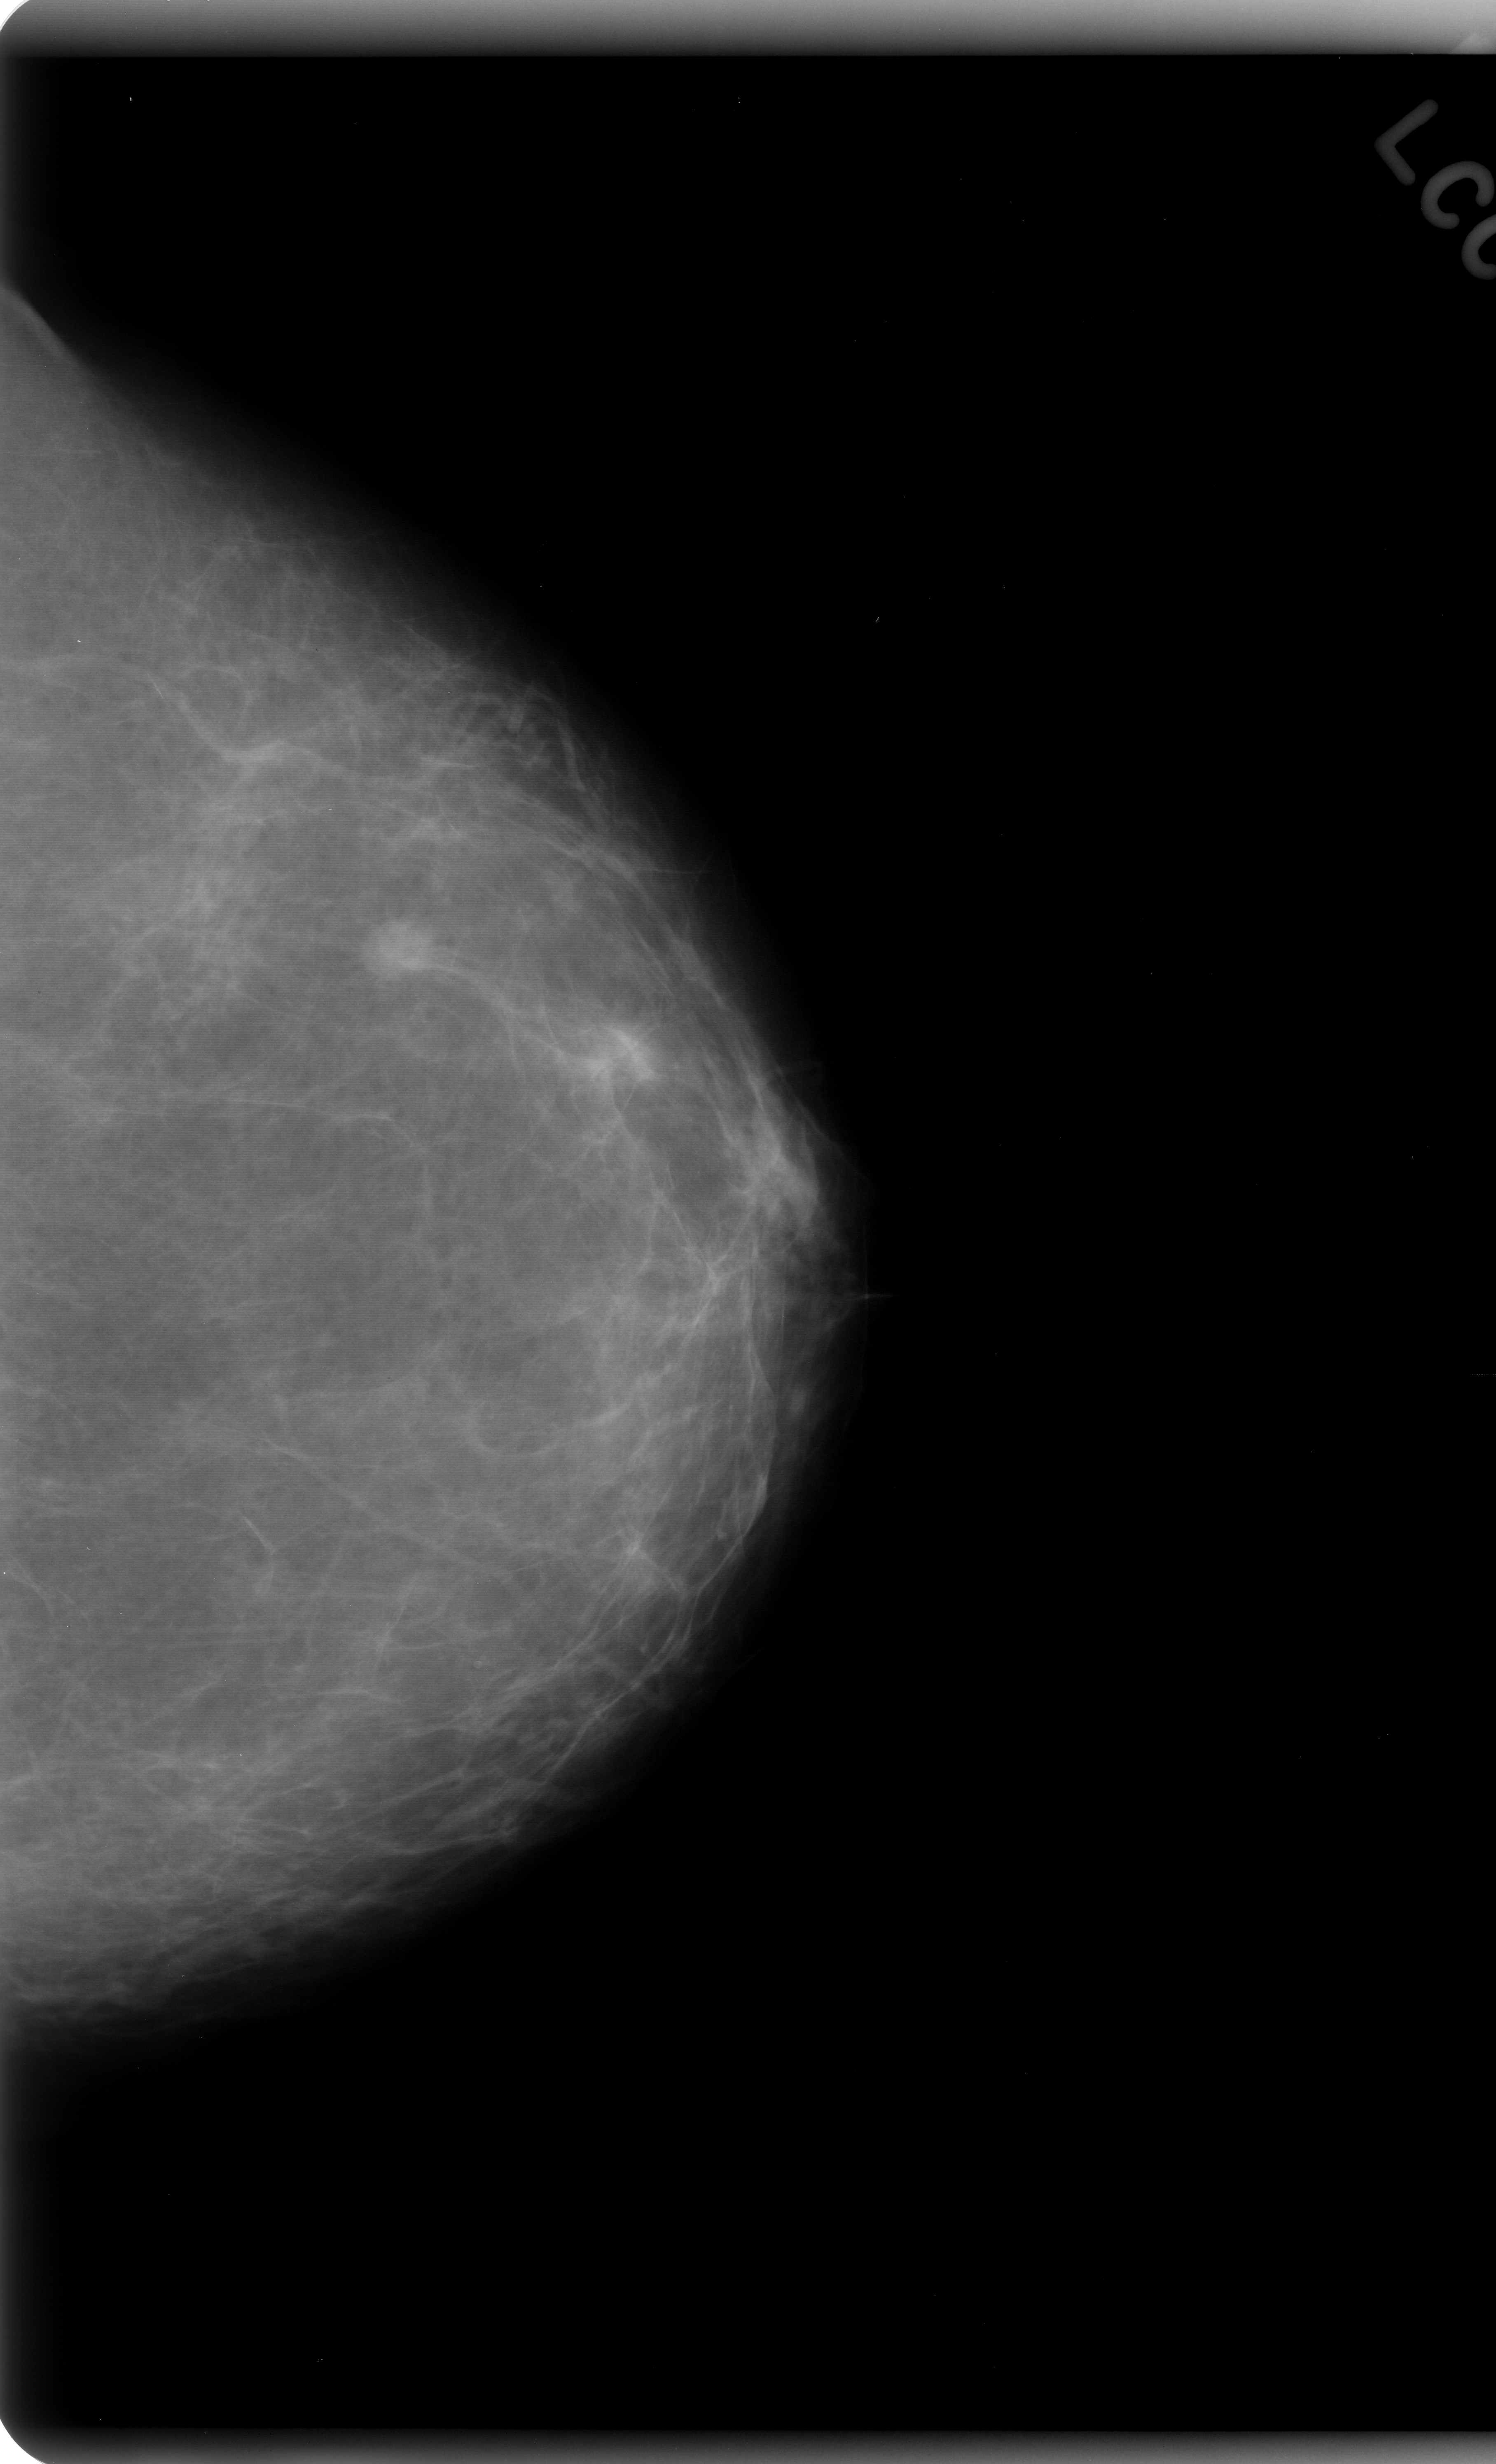
Mammogram (digitized film). Left breast. Craniocaudal (CC) view. Breast composition: almost entirely fatty (BI-RADS density category 1 of 4). 1496 × 2464 image matrix.
Expert-marked regions of interest on this image (one box per marked abnormality):
- mass, shape round, margins spiculated; BI-RADS assessment category 5; pathology (as recorded): malignant: box from (x=352, y=908) to (x=467, y=991) px